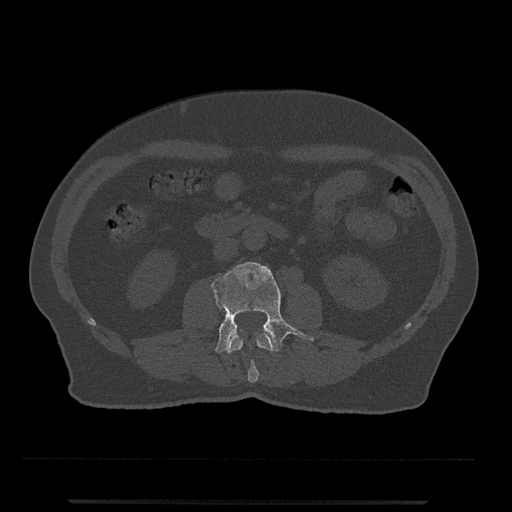
CT including the spine, one axial slice; slice 222 of 797 in the series (ordered by position); bone window (W 1800 / L 400 HU); 0.5 mm slice thickness; 512 × 512 image matrix, field of view 419 × 419 mm. Male patient, age 63 years. From the clinical record (not read from this slice): primary cancer: prostate.
Annotated regions visible in this slice (semi-automatic segmentation, software-assisted and operator-edited):
- L2 vertebra: bounding box <227,332,274,383> (left, top, right, bottom; pixels)
- L3 vertebra: <210,262,314,353>